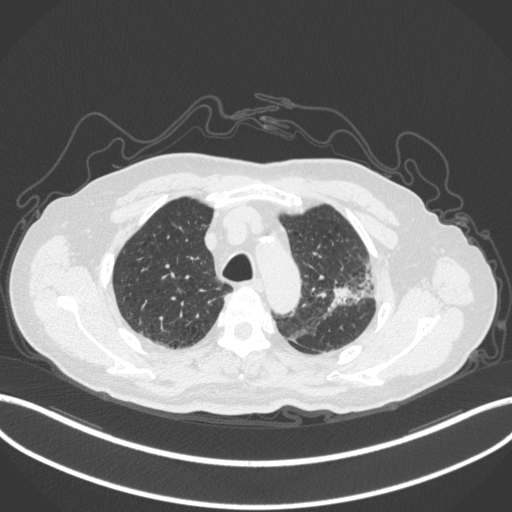
Chest CT, one axial slice; 120 kVp; lung window (W 1500 / L -600 HU); 1 mm slice thickness; 512 × 512 image matrix, field of view 400 × 400 mm. Patient: male, 79 years. Case-level facts recorded for this patient, not image findings: clinical TNM (as recorded): T2a N1 M1; histopathological grade: G3.
Outlined on this slice (bounding box drawn by a radiologist):
- lung tumour (recorded histology: adenocarcinoma): bounding box (x1, y1, x2, y2) in pixels: (322, 278, 376, 314)